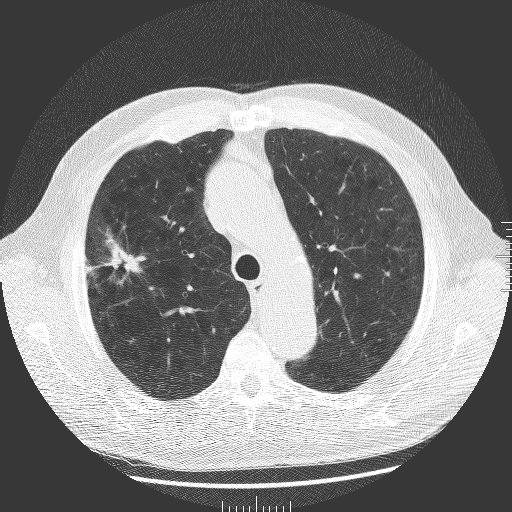
Low-dose screening chest CT, one axial slice. Slice 138 of 181 in the series (ordered by position). Reconstruction kernel BONE. Lung window (W 1500 / L -600 HU). 2 mm slice thickness. 512 × 512 image matrix, field of view 380 × 380 mm.
Annotated regions visible in this slice (outlined manually by an expert reader):
- lesion 1 (tumor, upper lobe of right lung): box from (x=106, y=236) to (x=141, y=273) px